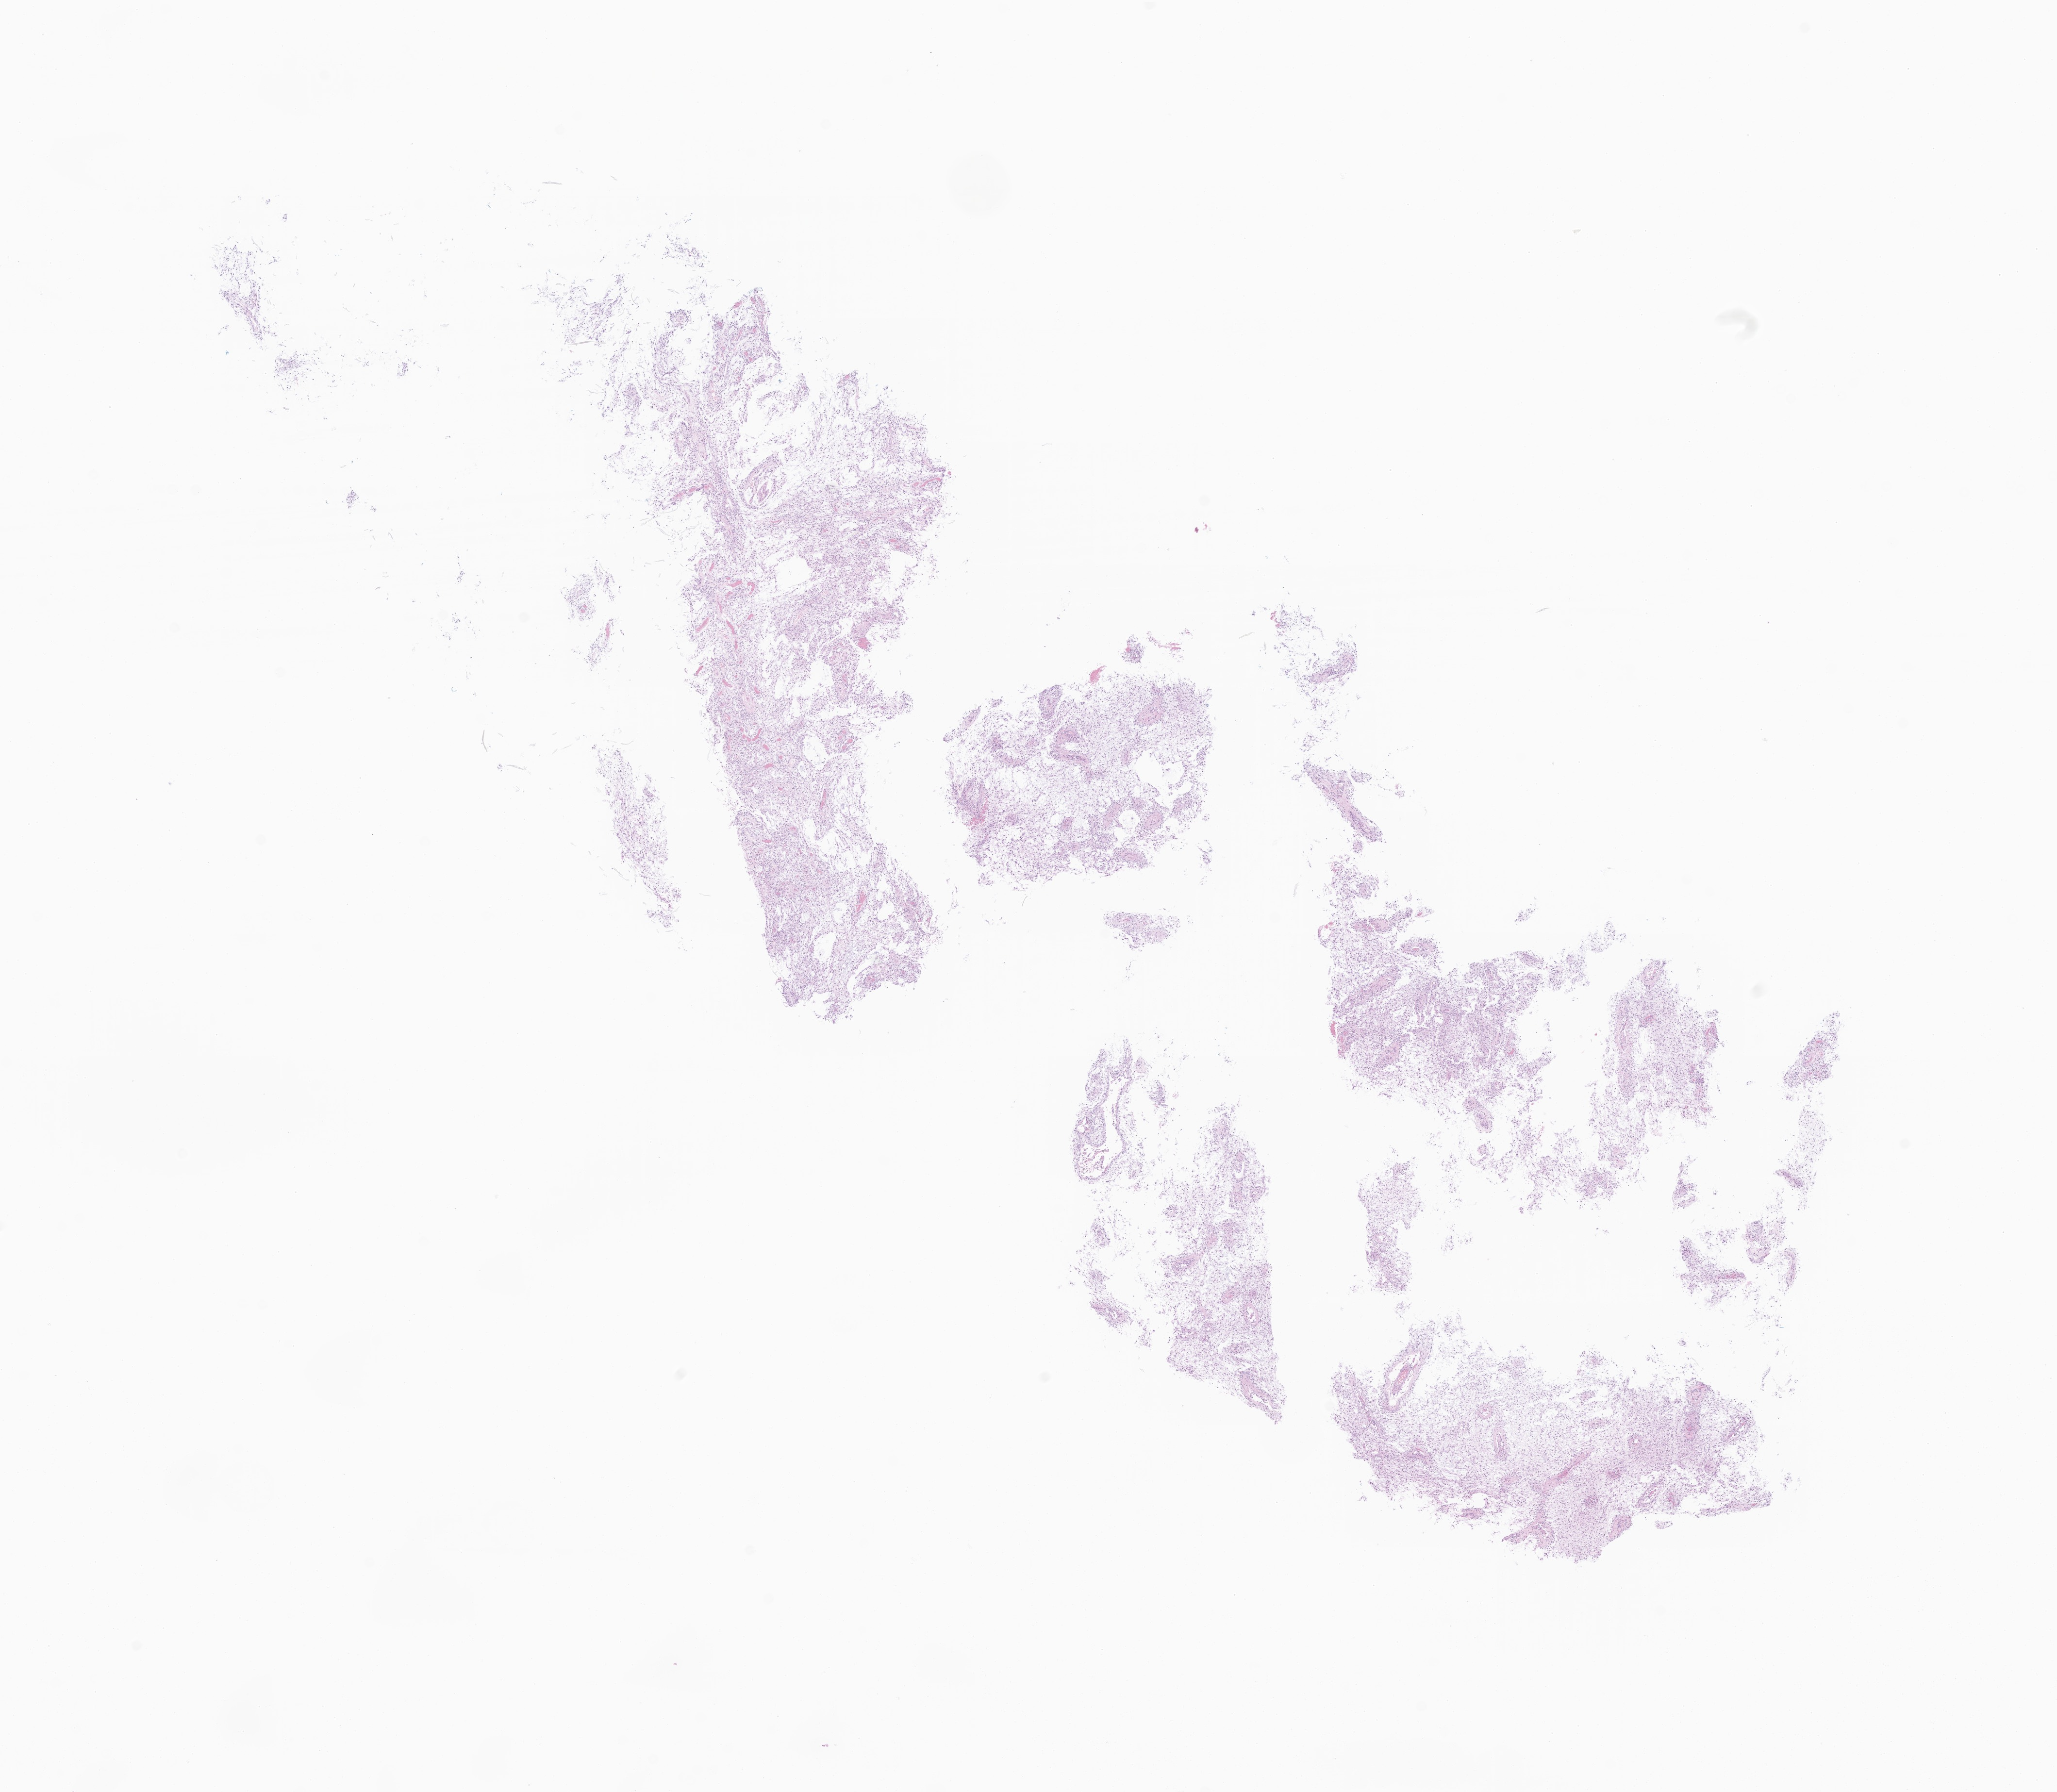
Haematoxylin and eosin whole-slide image of tumor tissue from the brain — a low-resolution overview of the entire scanned area, about 17.9 x 15.6 mm. Formalin-fixed, paraffin-embedded (FFPE) tissue. Patient: female, age 36 months (3 years).
Diagnosis: Pilocytic astrocytoma.